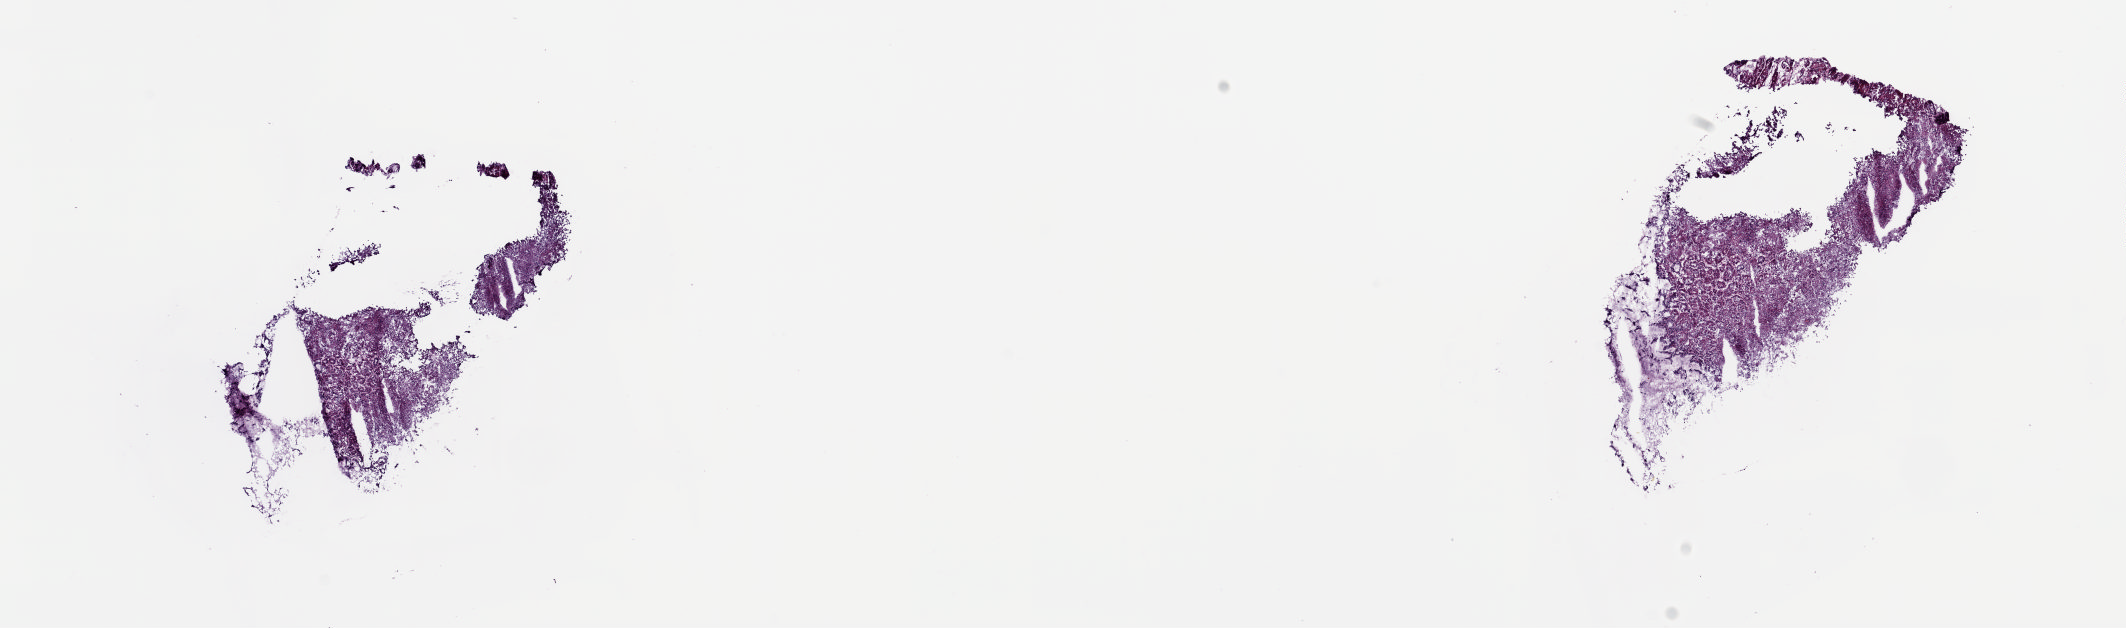
Digitized H&E tissue section (whole slide) — a low-resolution overview of the entire scanned area, about 16.9 x 5.0 mm, frozen section from the top of the tissue portion, esophagus, solid tissue normal (non-tumour tissue) sample. Male, age 67 years at initial diagnosis. Slide review estimates, as recorded: tumour cells 0%, tumour nuclei 0%, normal cells 70%, stromal cells 30%, necrosis 0%. Inflammatory infiltration, as recorded: lymphocyte infiltration 0%, monocyte infiltration 0%, neutrophil infiltration 0%.
• this section: solid tissue normal sample (biorepository sample class)
• patient diagnosis: Adenocarcinoma, NOS (lower third of esophagus)